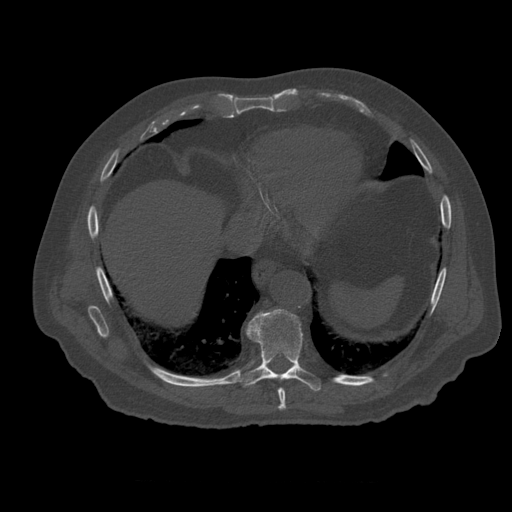
CT including the spine, one axial slice; slice 324 of 399 in the series (ordered by position); reconstruction kernel STANDARD; 120 kVp; bone window (W 1800 / L 400 HU); 1.25 mm slice thickness; 512 × 512 image matrix, field of view 407 × 407 mm. Patient age 73 years. Case-level facts recorded for this patient, not image findings: primary cancer: prostate; vertebrae with lytic lesions (as recorded): L2.
Structures marked on this image (semi-automatically segmented with operator editing):
- T8 vertebra: bounding box [x1, y1, x2, y2] px = [278, 389, 287, 411]
- T9 vertebra: [236, 309, 322, 391]